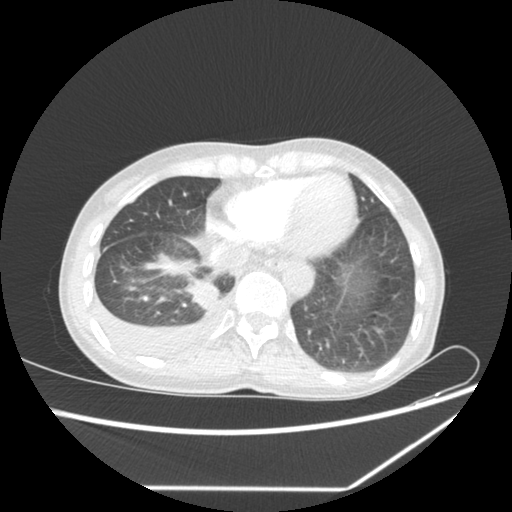
Chest CT, one axial slice; slice 1 of 1 in the series (ordered by position); 80 kVp; lung window (W 1500 / L -600 HU); 512 × 512 image matrix, field of view 364 × 364 mm. Female patient, age 59 years. Case-level facts recorded for this patient, not image findings: clinical TNM (as recorded): T1c N1 M1.
Outlined on this slice (rectangle marked by the reading radiologist):
- lung tumour (recorded histology: adenocarcinoma): box from (x=184, y=276) to (x=219, y=312) px